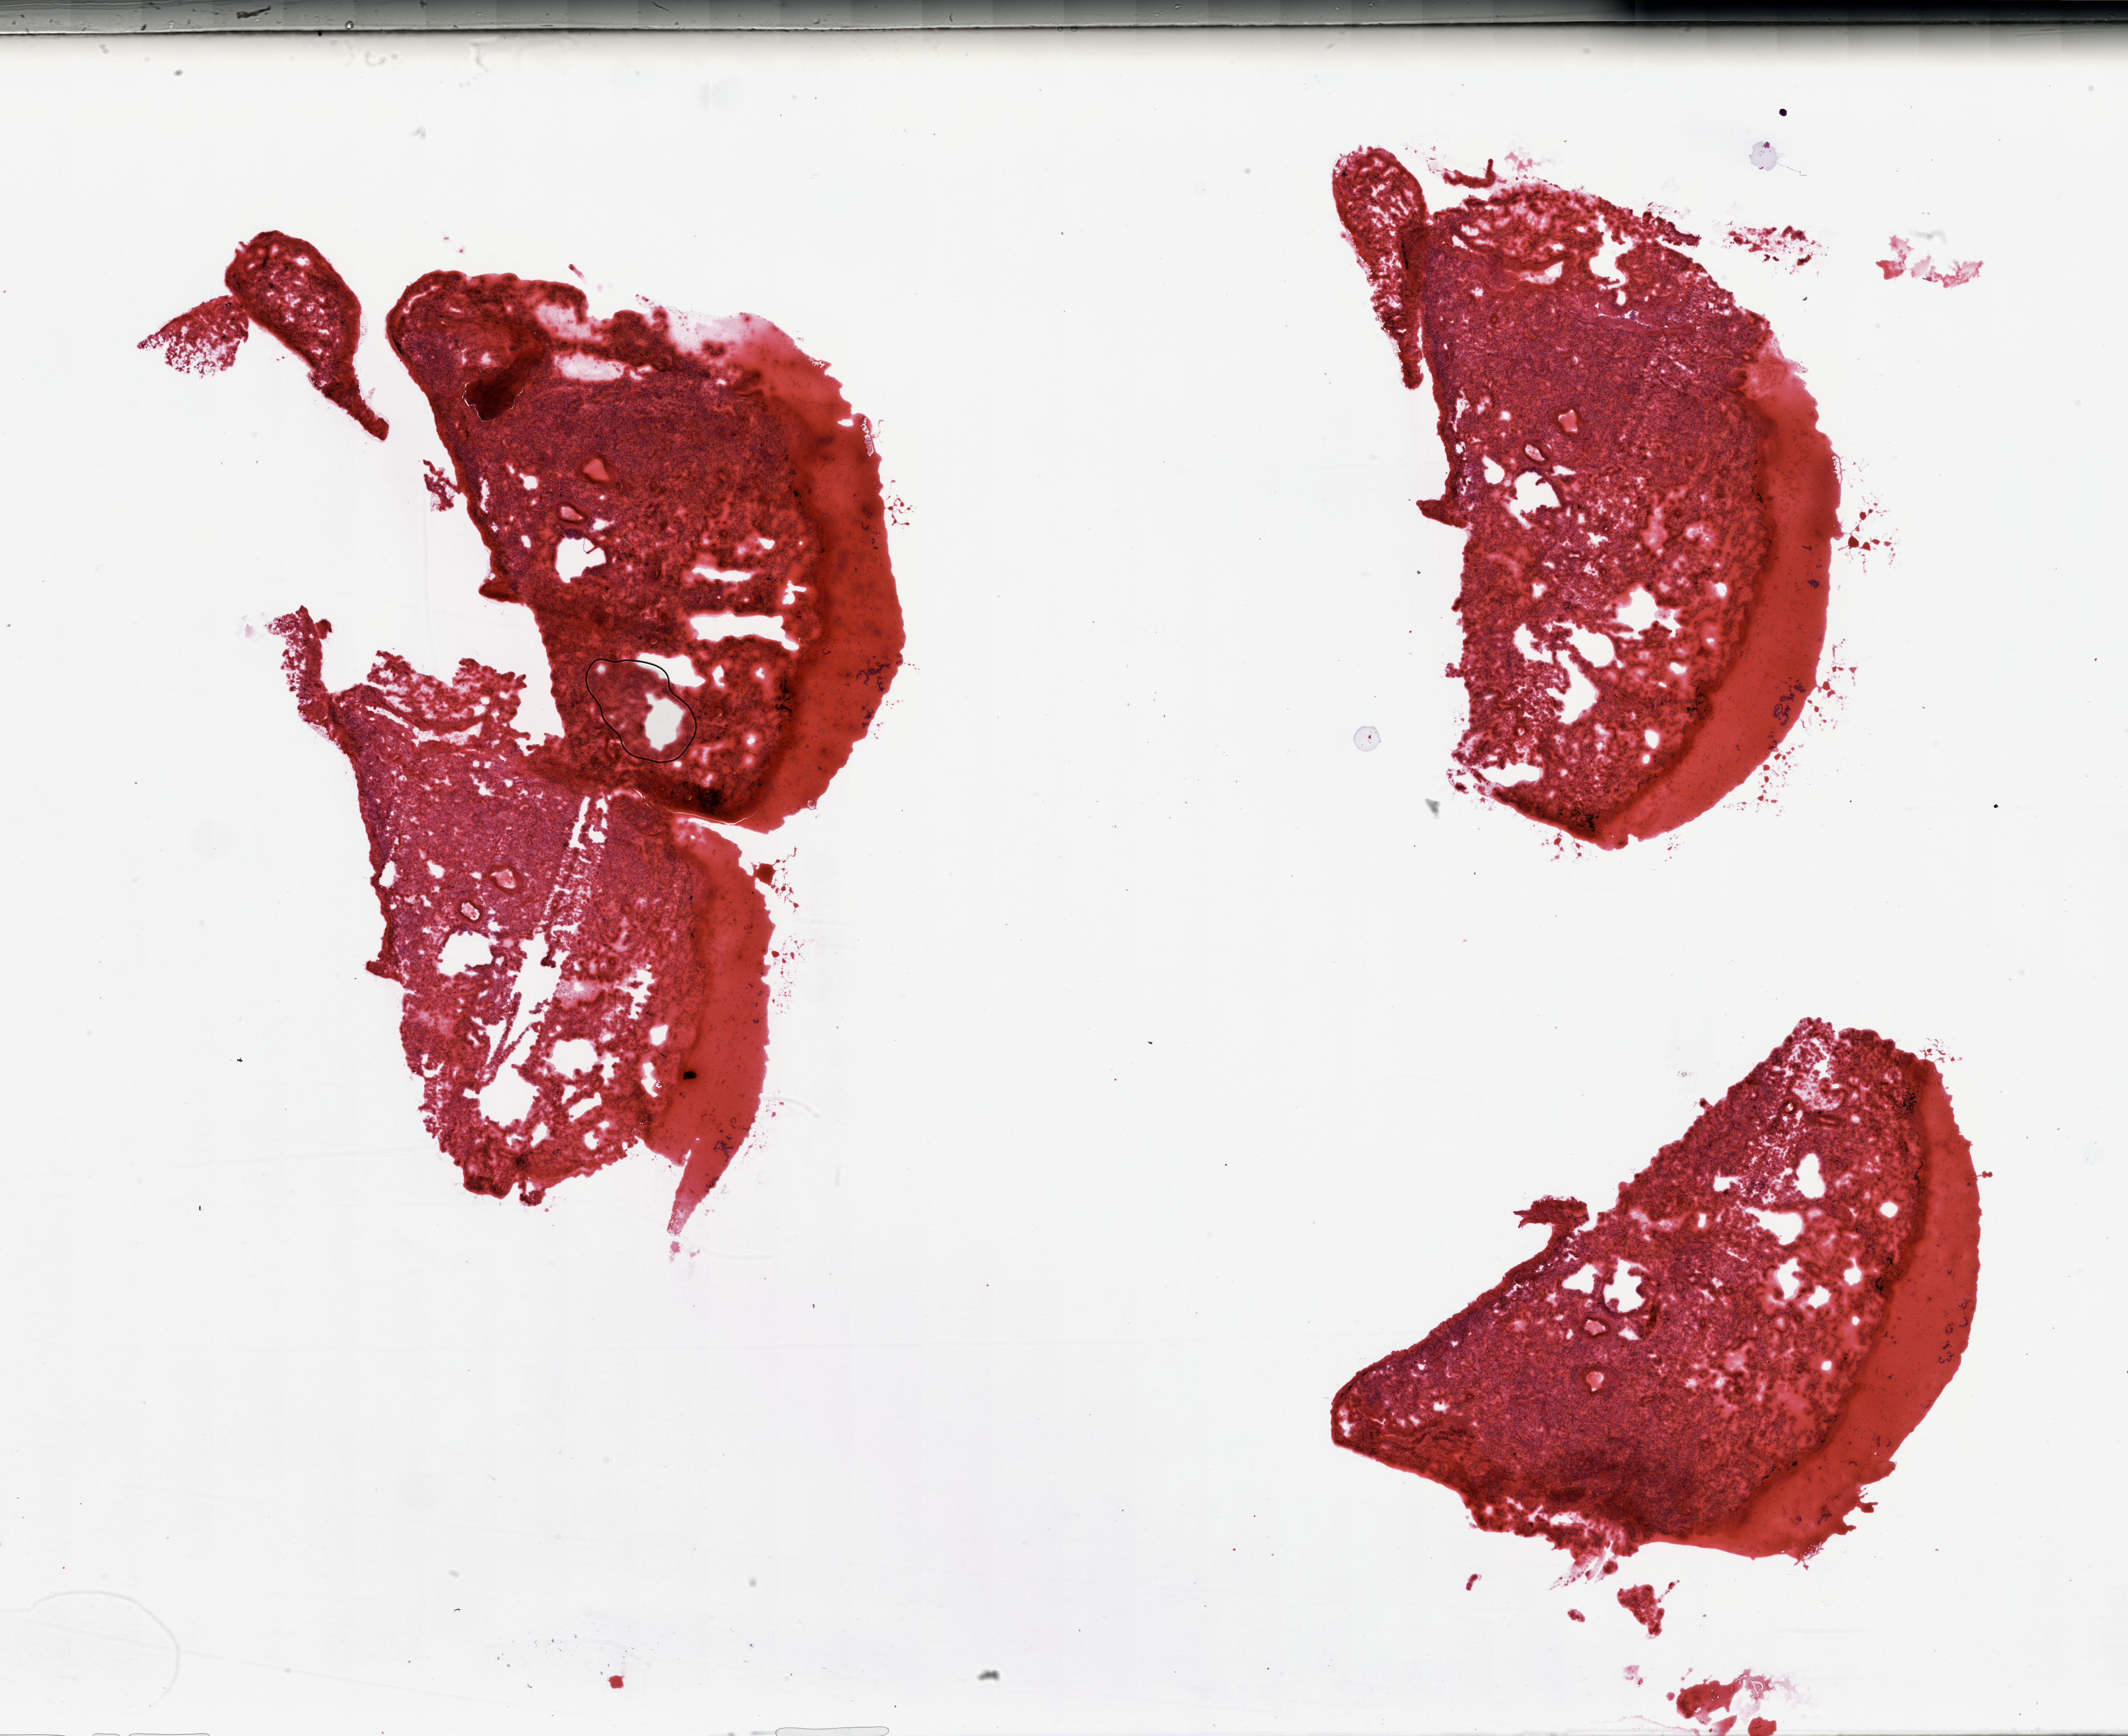
Hematoxylin and eosin (H&E) stained whole-slide image, whole scanned area (about 29.5 x 24.1 mm) shown as a low-resolution overview; normal (non-tumour) tissue sample, sampled site: lung. Patient: male, age 73 years.
This section: normal (non-tumour) tissue from the same patient. Patient diagnosis: Adenocarcinoma, NOS.